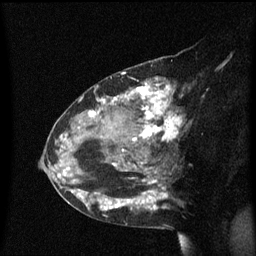
Breast MRI (dynamic contrast-enhanced), one sagittal slice; position 36 of 60 along the scan axis; dynamic contrast-enhanced series, image 2 of 3 at this slice position (ordered by acquisition); 1.5 T; TE 4.2 ms, TR 8.4 ms; 2 mm slice thickness; 256 × 256 image matrix, field of view 200 × 200 mm. Female patient, age 48 years. From the clinical record (not read from this slice): setting: breast cancer imaged before/during neoadjuvant chemotherapy; receptor status: HR-positive, HER2-negative.
Annotated regions visible in this slice (semi-automatic segmentation, software-assisted and operator-edited):
- analysis volume of interest (the breast-tissue region the enhancement analysis was run in; not a lesion): bounding box (x1, y1, x2, y2) in pixels: (80, 78, 187, 221)
- tumour enhancement mask (voxels above the 70 % enhancement threshold inside the analysis volume of interest): (80, 79, 183, 211)